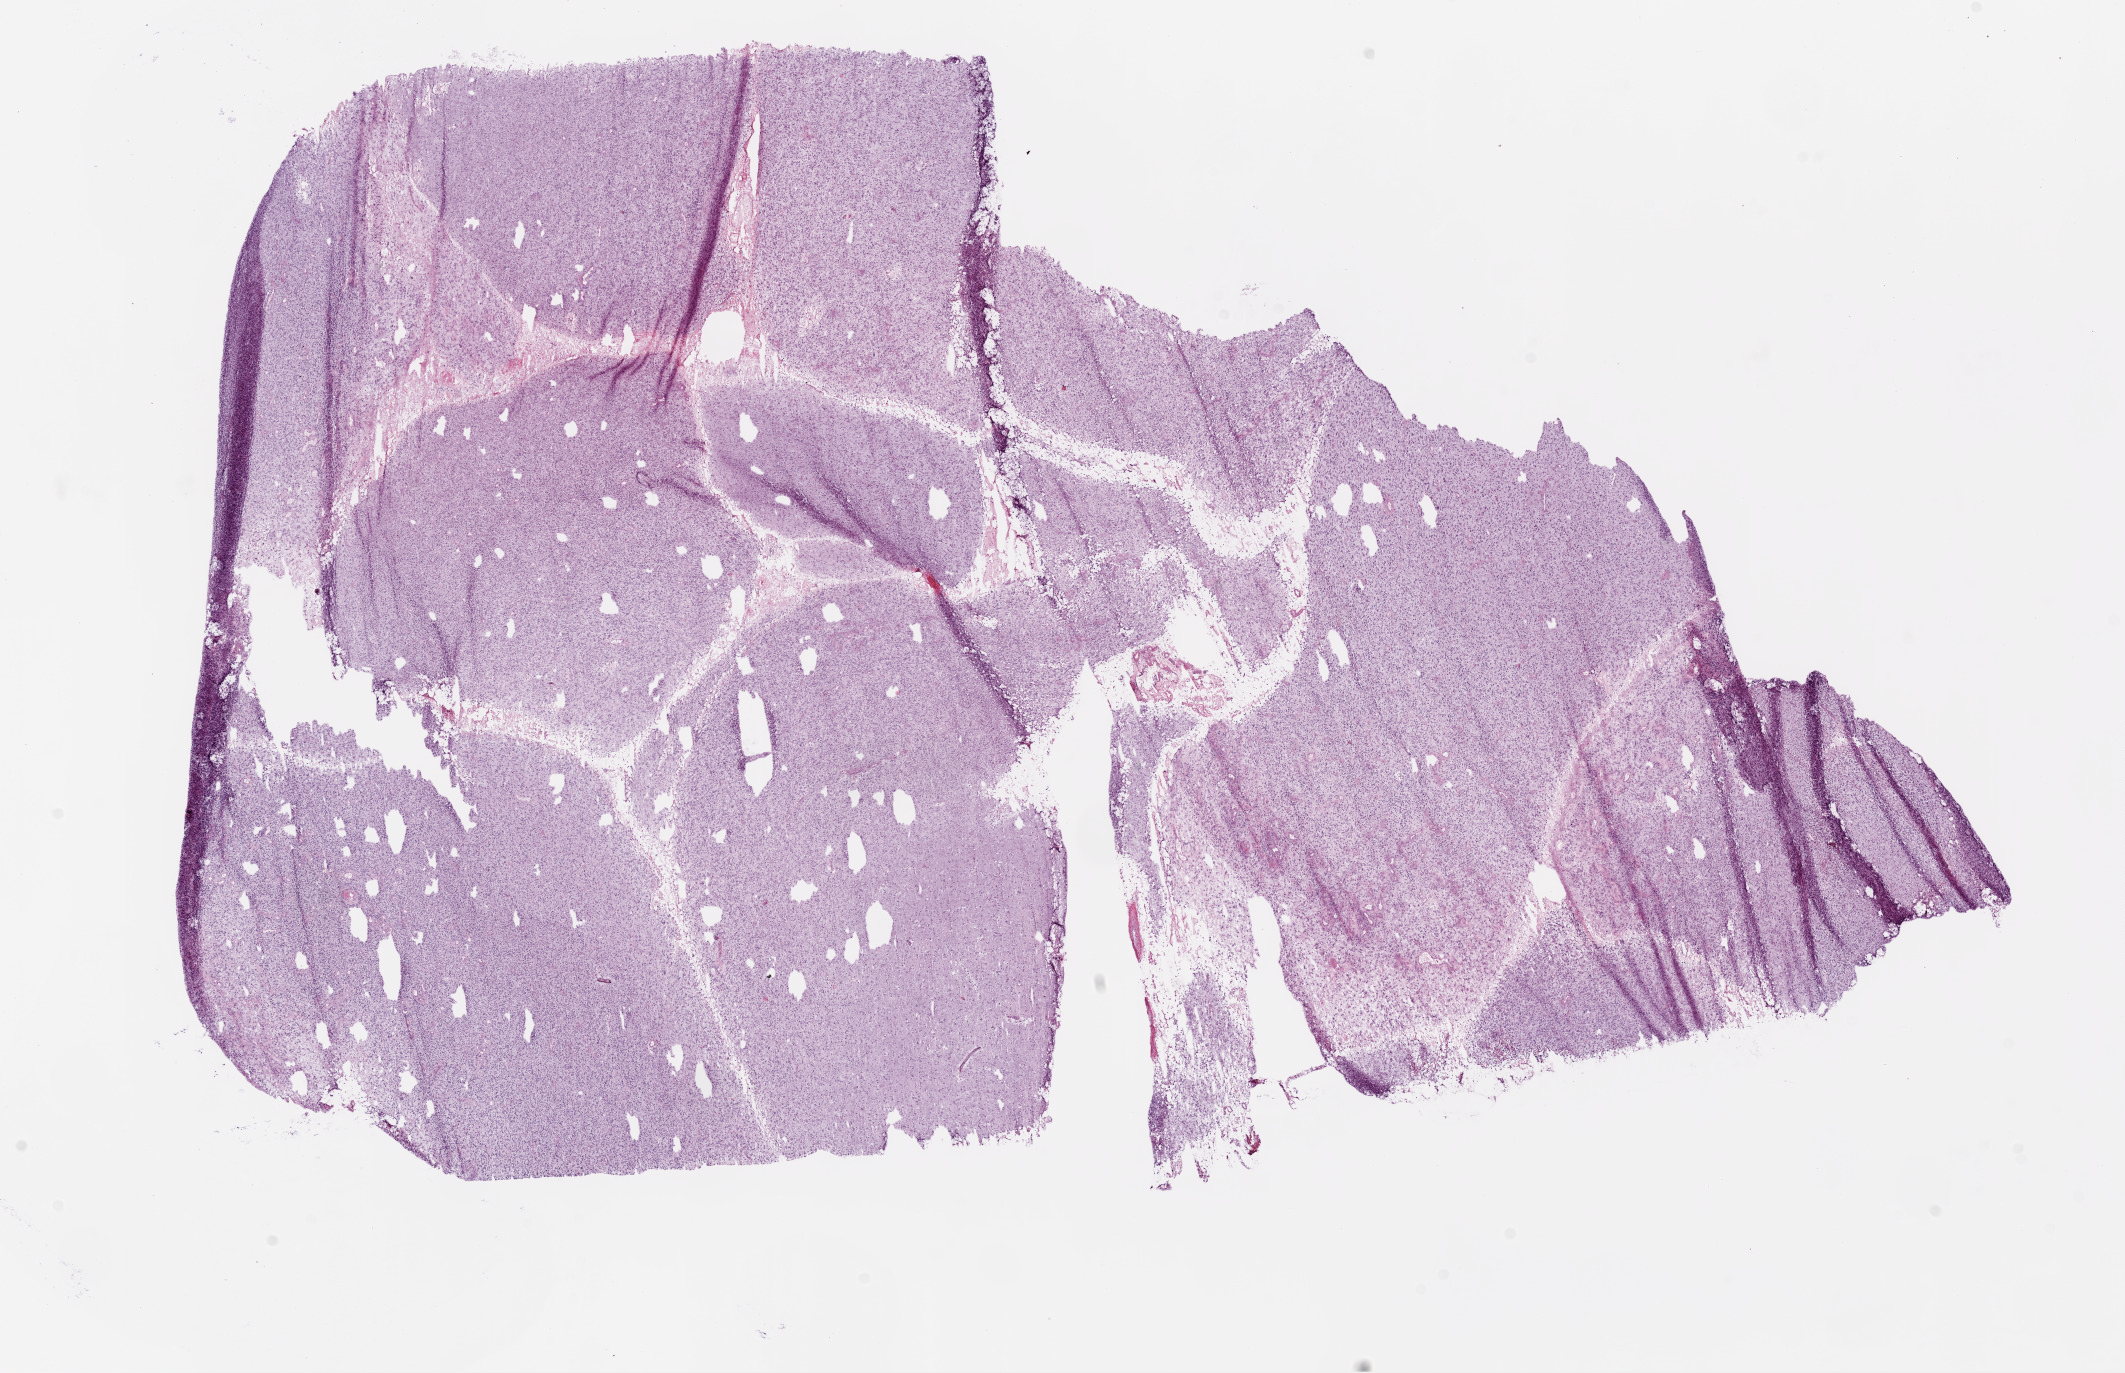
Digitized Hematoxylin and eosin (H&E) stained tissue section (whole slide) — whole scanned area (about 17.1 x 11.0 mm, from a 20x scan) shown as a low-resolution overview, frozen section from the bottom of the tissue portion, brain, primary tumour sample. Female, age 21 years at initial diagnosis.
Diagnosis: Glioblastoma.